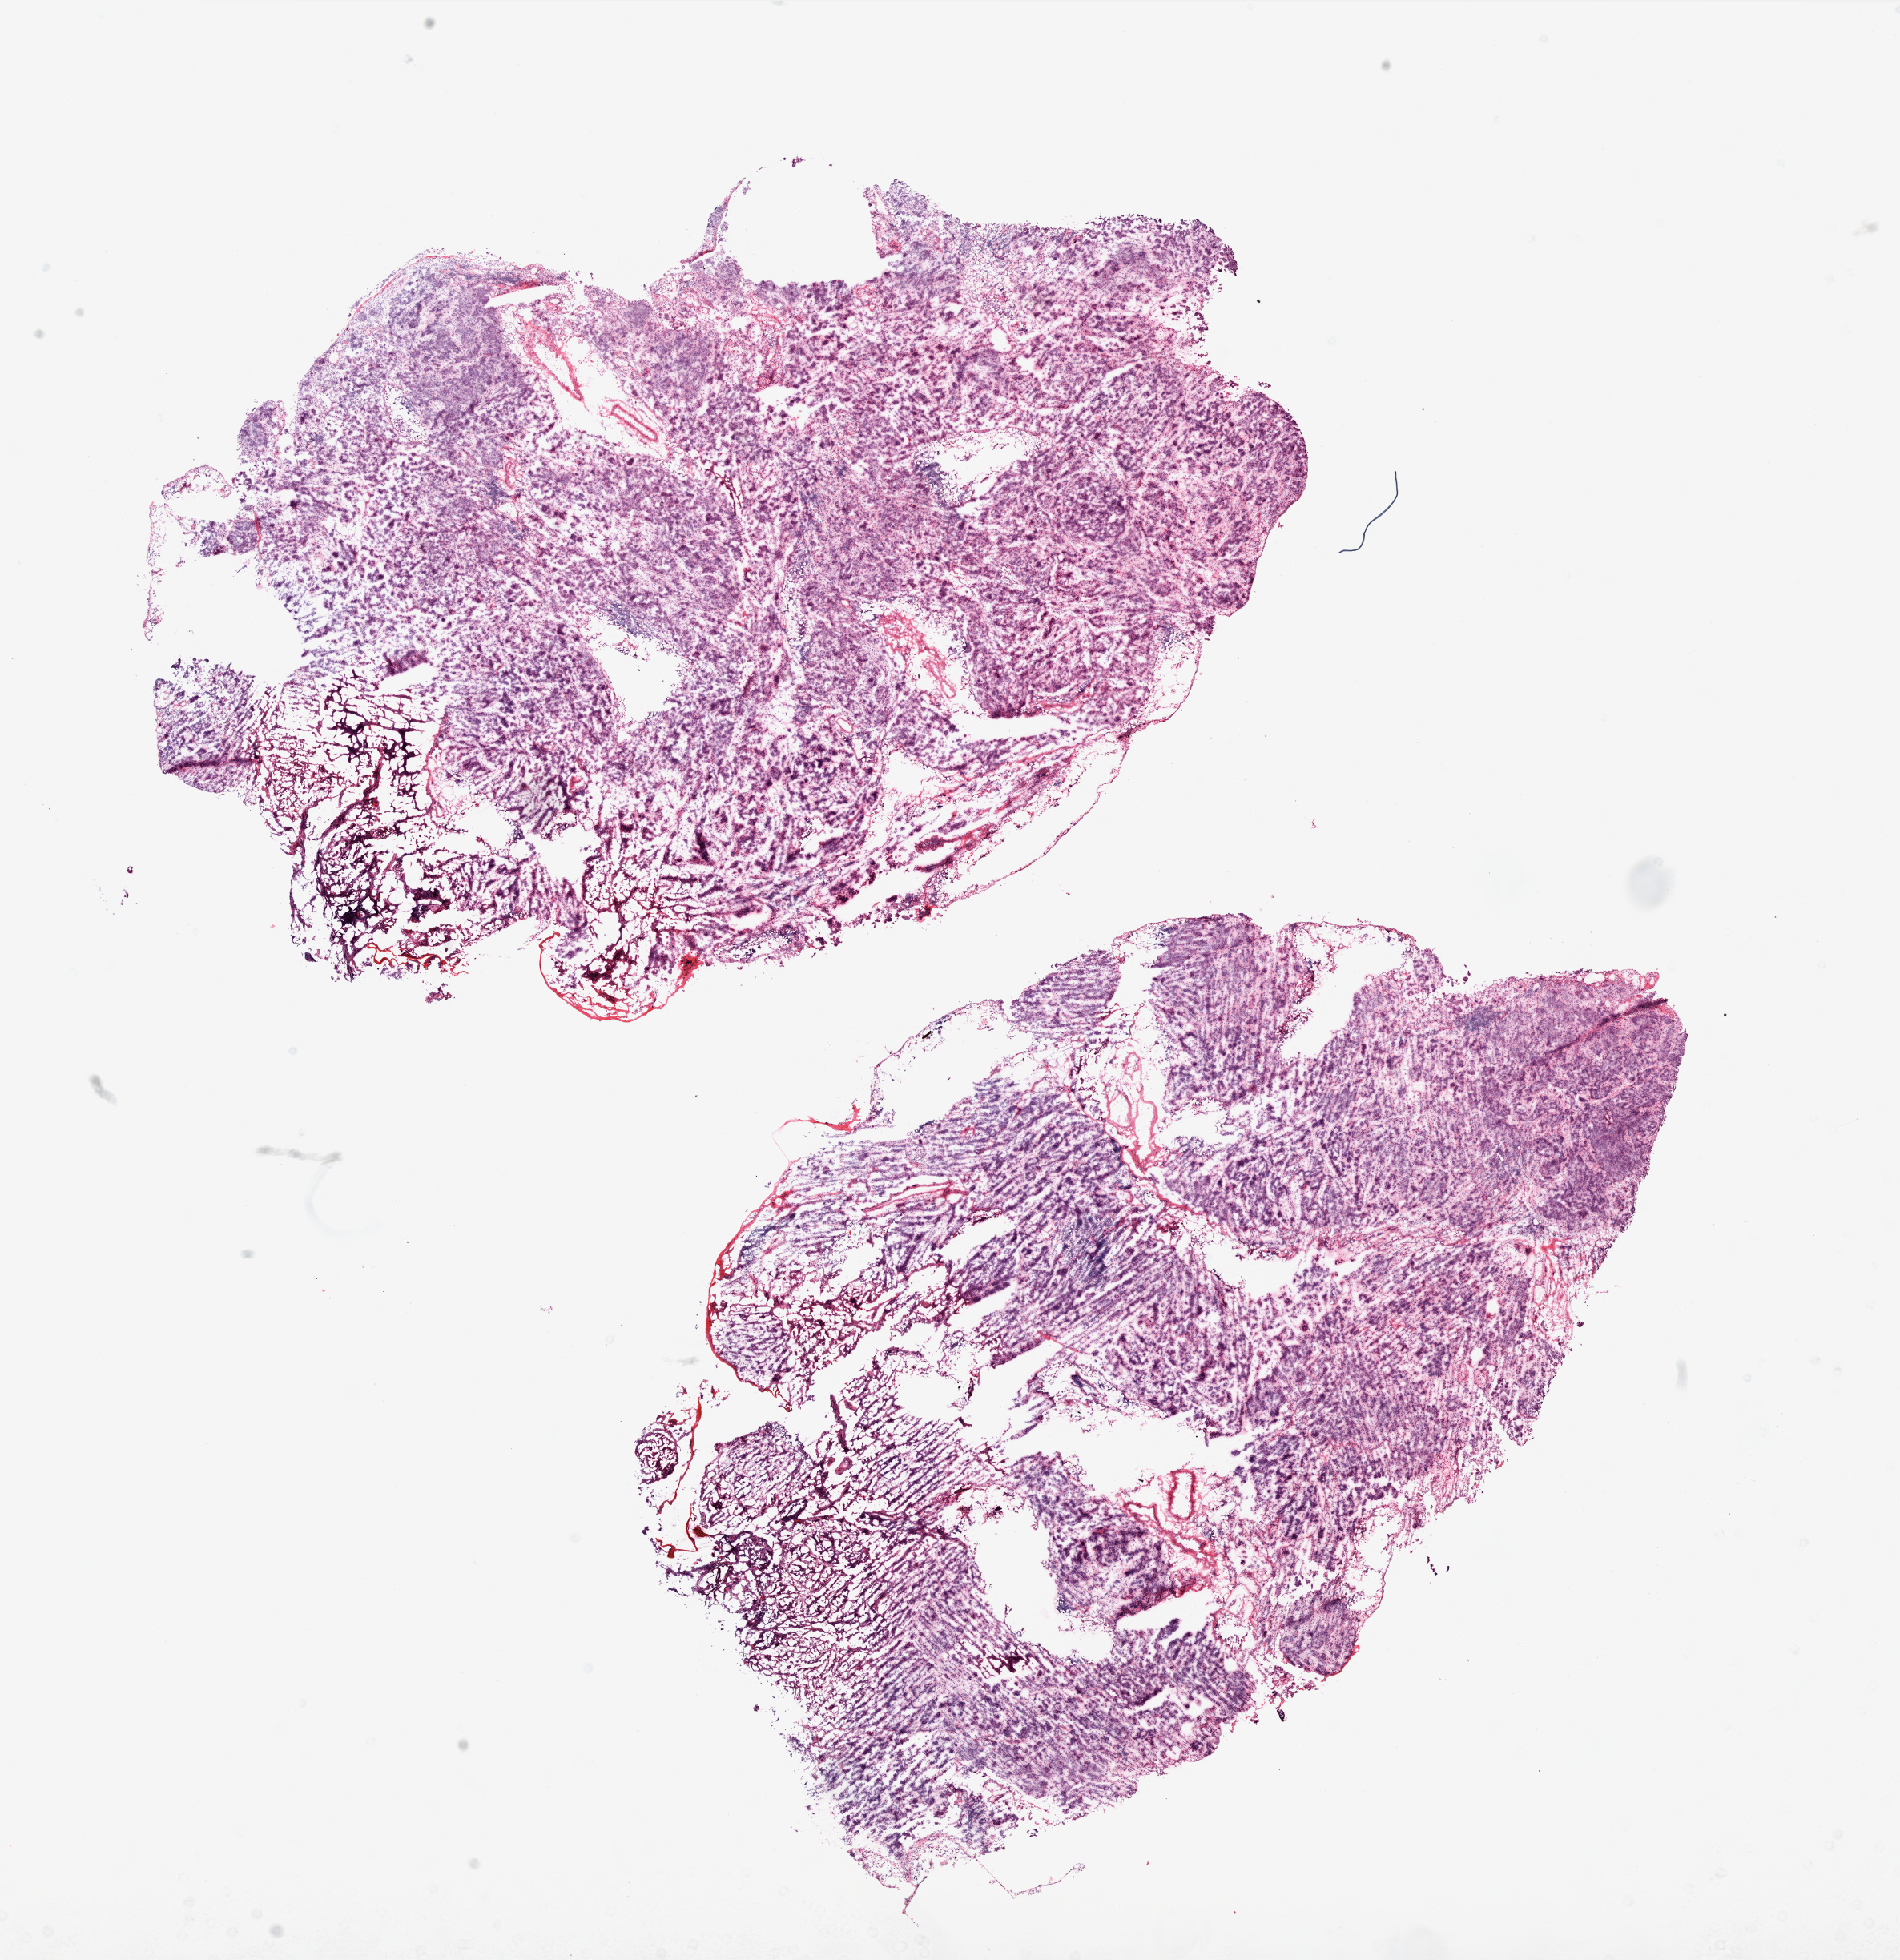
Digitized H&E tissue section (whole slide) — whole scanned area (about 19.0 x 19.6 mm, acquisition: 20x scan) shown as a low-resolution overview, frozen section, ovary, primary tumour sample. Patient: female, age at initial diagnosis 45 years. Histologic grade: G3 (poorly differentiated). Slide review estimates, as recorded: tumour cells 75%, tumour nuclei 80%, normal cells 0%, stromal cells 25%, necrosis 0%.
FIGO stage: IV. Pathologic diagnosis: Serous cystadenocarcinoma, NOS.